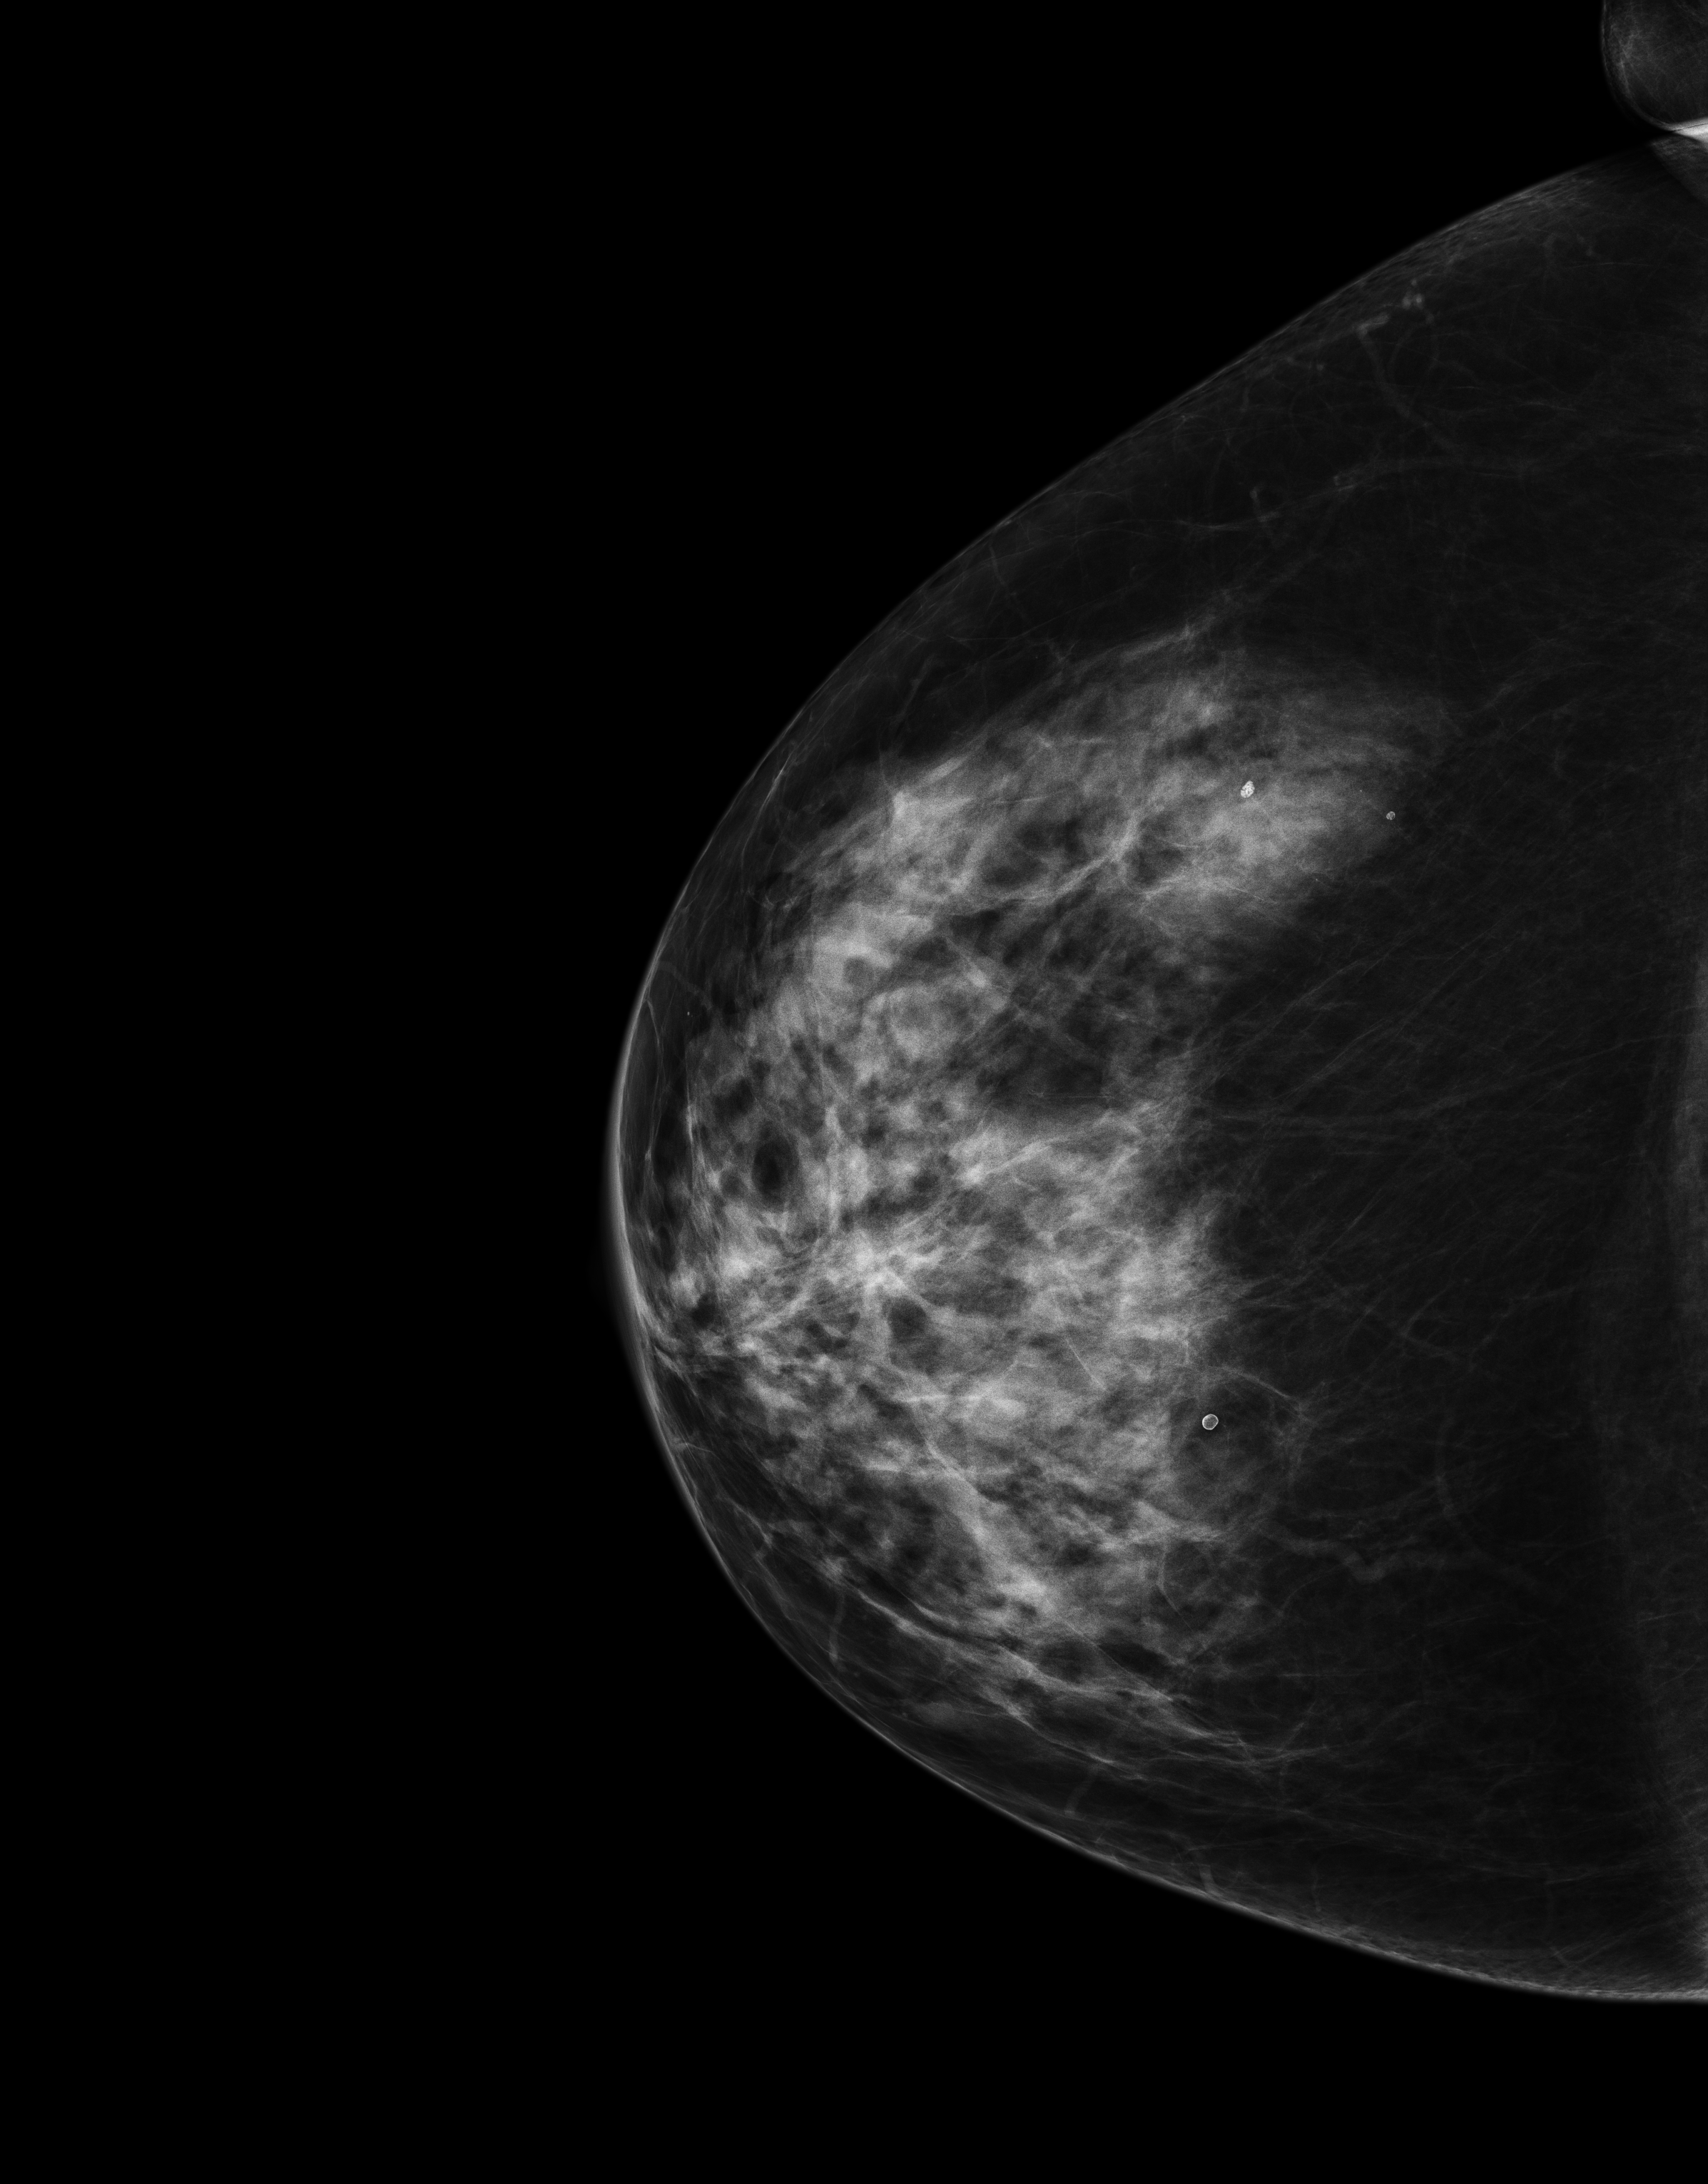
Full-field digital mammogram (FFDM); right breast; CC view; annual screening mammography examination; system: Senographe Essential ADS_56.21.3. Patient: female, 65 years.
BI-RADS breast density category at the screening exam (both breasts, scale 1–4): 3. Final BI-RADS category for the screening round (tomosynthesis exam, both breasts): category 1. Recall: no recall after this screen.